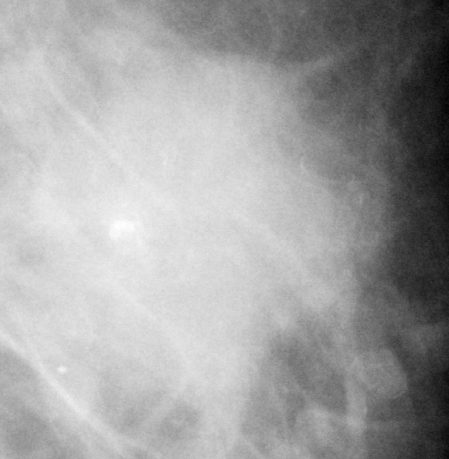
Crop from a digitized film mammogram around one marked abnormality, left breast, MLO view, BI-RADS breast density category 2 (scale 1–4).
Marked abnormality: mass, shape irregular, margins ill defined / spiculated; BI-RADS assessment category 4; subtlety rating 5 on a 1 (subtle) to 5 (obvious) scale; pathology (as recorded): malignant.